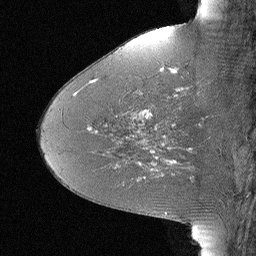
Breast MRI (dynamic contrast-enhanced), one sagittal slice; slice 26 of 64 in the series (ordered by position); dynamic contrast-enhanced study with each time point stored as its own series, time point 2 of 3 at this slice position (early post-contrast, ordered by acquisition time); 1.5 T; TE 4 ms, TR 30 ms; 2.25 mm slice thickness; 256 × 256 image matrix, field of view 180 × 180 mm. Patient: female, 46 years. From the clinical record (not read from this slice): setting: breast cancer imaged before/during neoadjuvant chemotherapy; receptor status: HR-positive, HER2-negative.
Outlined on this slice (semi-automatically segmented with operator editing):
- analysis volume of interest (the breast-tissue region the enhancement analysis was run in; not a lesion): box from (x=106, y=43) to (x=184, y=119) px
- tumour enhancement mask (voxels above the 90 % enhancement threshold inside the analysis volume of interest): (x=136, y=69)–(x=177, y=118)